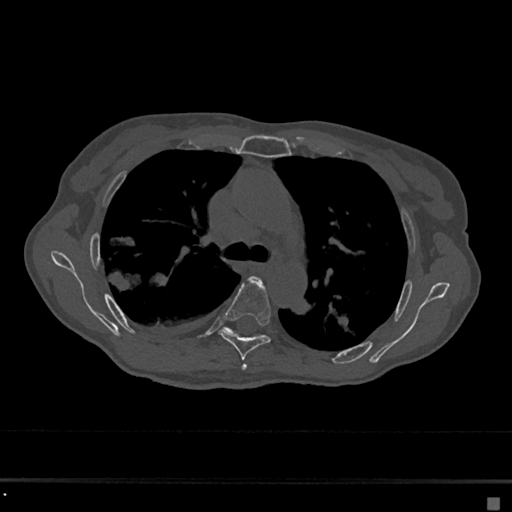
CT including the spine, one axial slice. Slice 458 of 797 in the series (ordered by position). Reconstruction kernel Br40s/3. Bone window (W 1800 / L 400 HU). 0.5 mm slice thickness. 512 × 512 image matrix, field of view 360 × 360 mm. Patient: female, 68 years. Case-level facts recorded for this patient, not image findings: primary cancer: renal.
Outlined on this slice (semi-automatically segmented with operator editing):
- T4 vertebra: bounding box (x1, y1, x2, y2) in pixels: (242, 281, 263, 371)
- T5 vertebra: (219, 279, 271, 360)
- T6 vertebra: (225, 328, 264, 337)